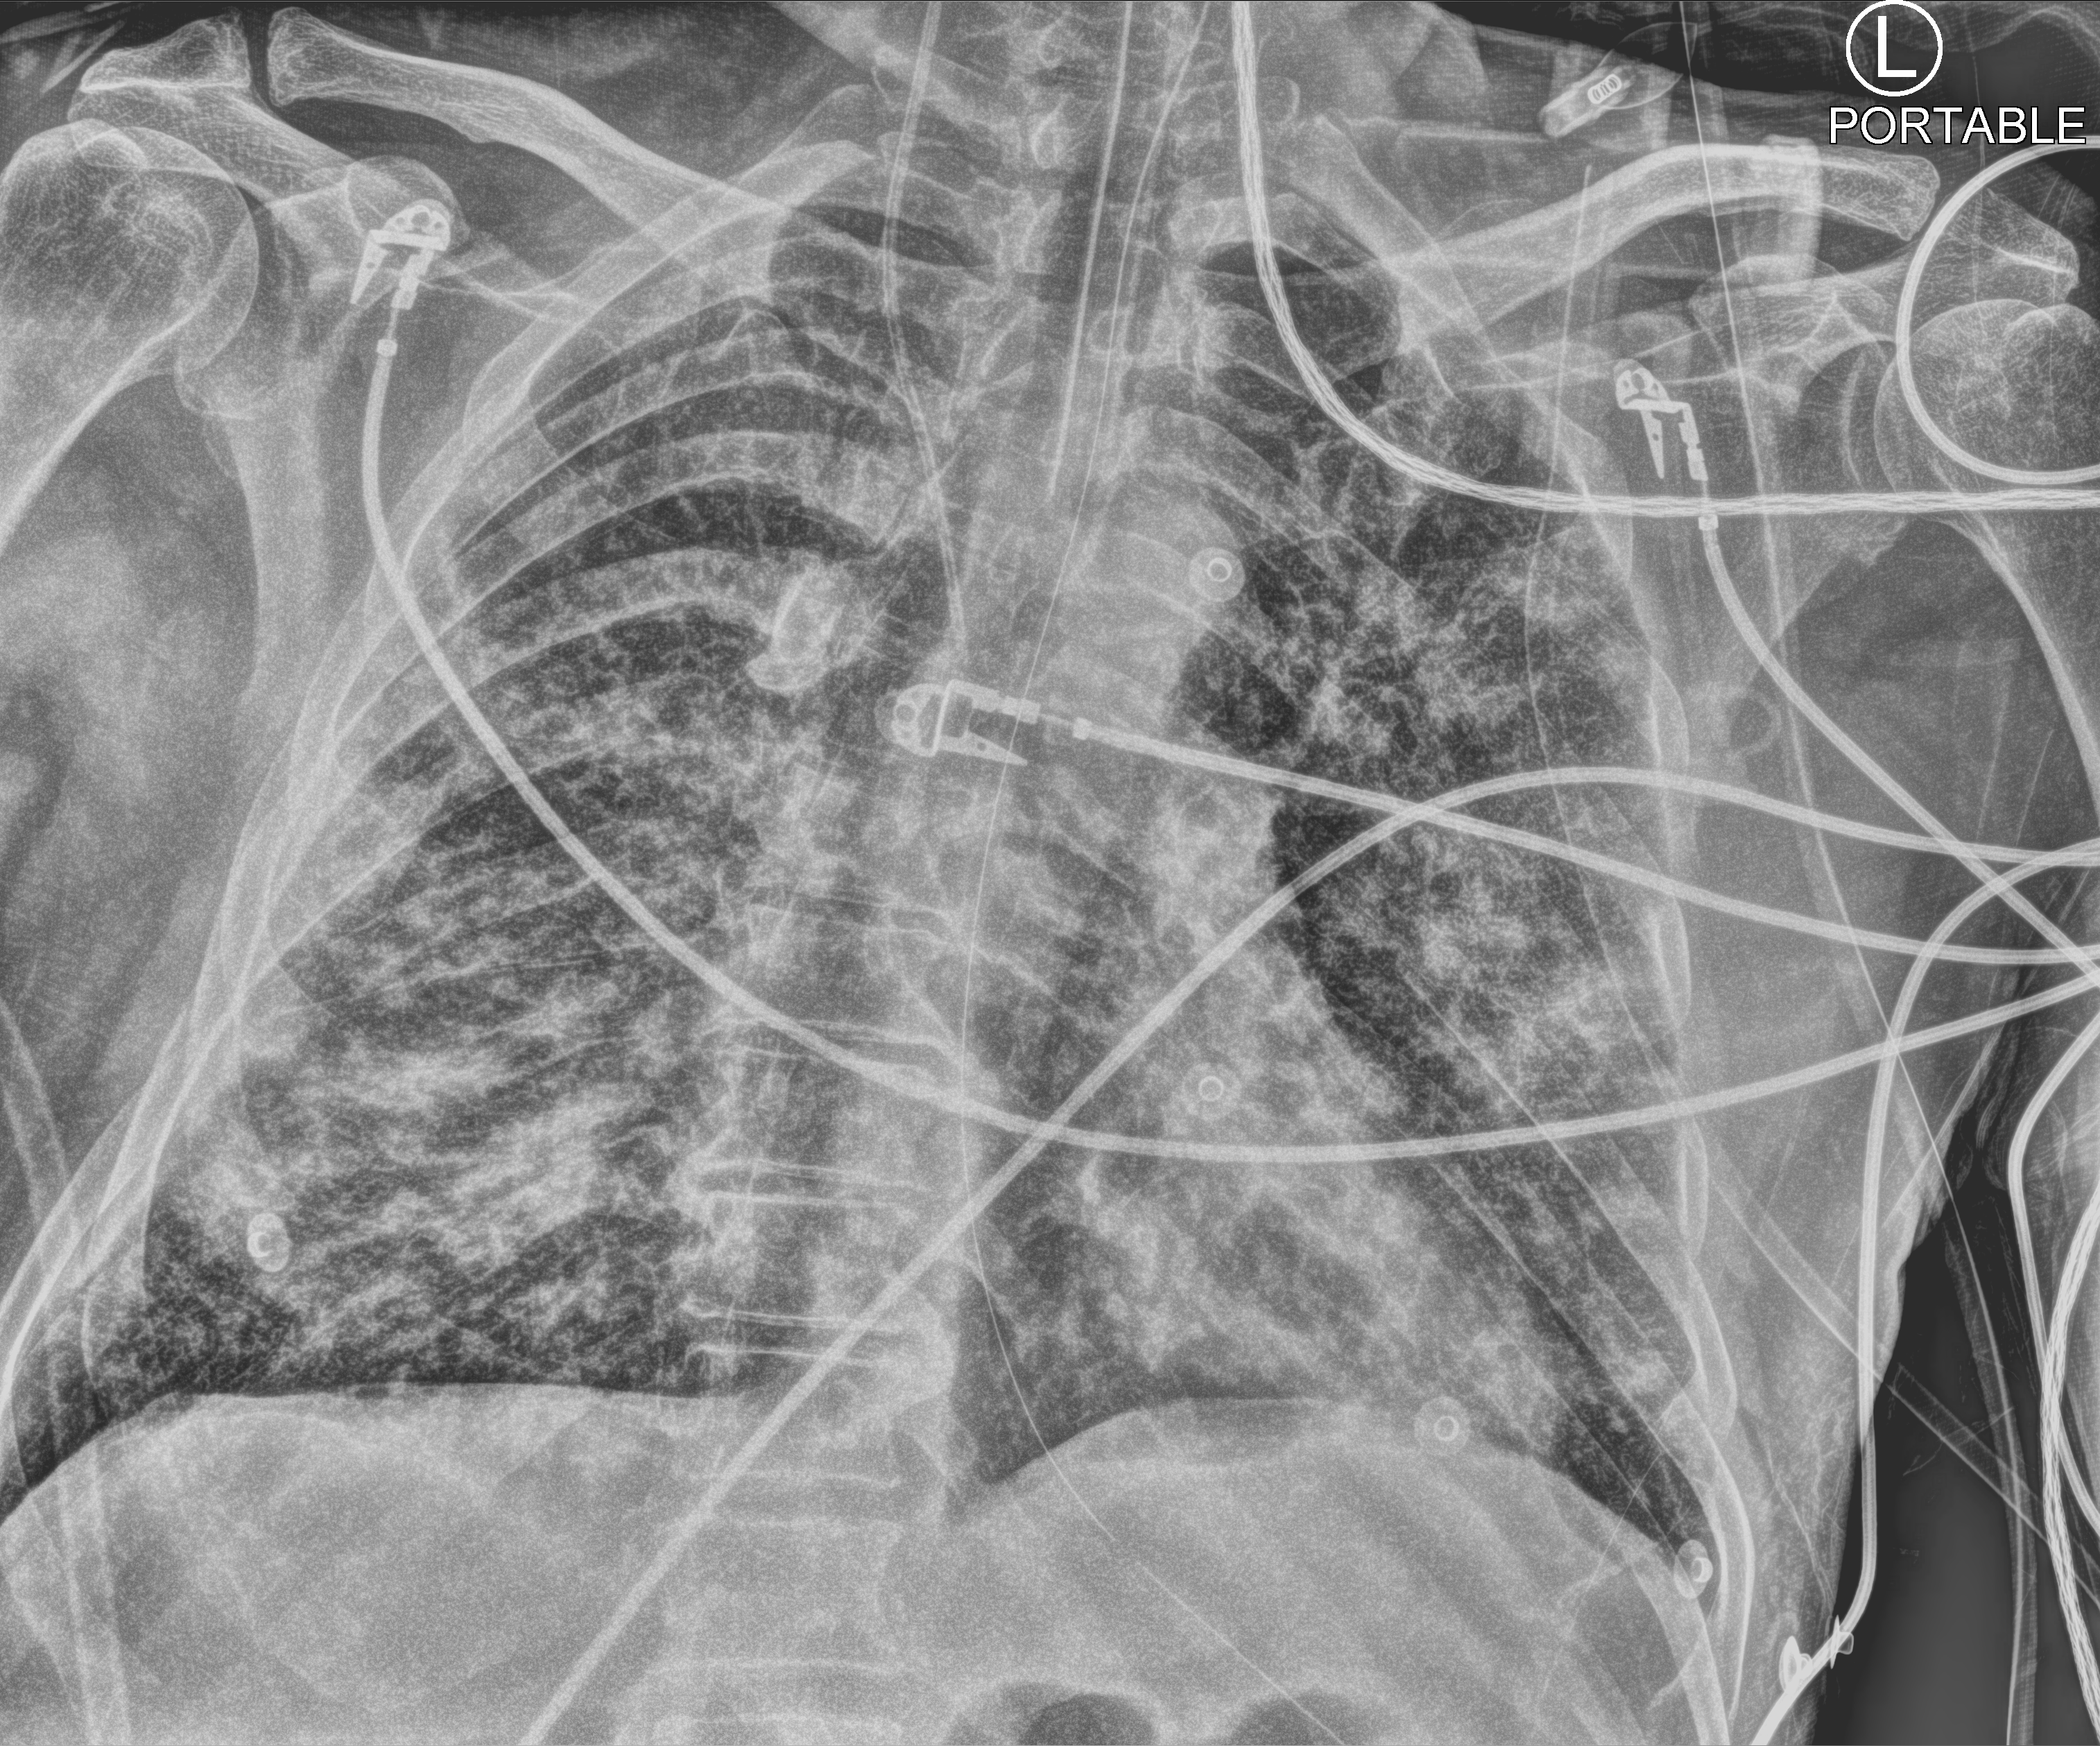
Bedside chest radiograph (computed radiography); anteroposterior (AP) projection. Male patient hospitalised with COVID-19, age 60–74 years.
From the hospital-stay record, not from the radiograph (when in the stay this image was taken is not recorded):
- hypertension (admission record): yes